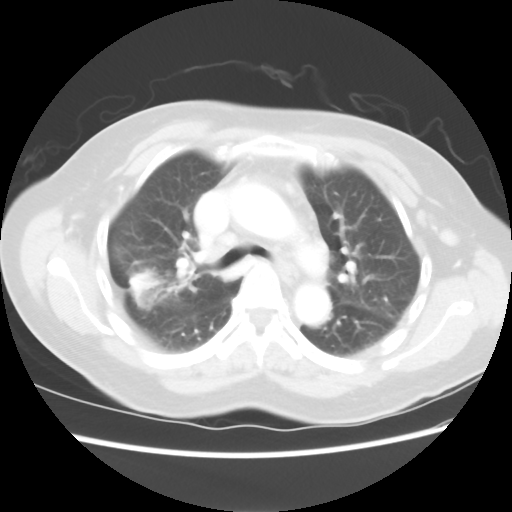
Chest CT, one axial slice. Slice 47 of 80 in the series (ordered by position). Reconstruction kernel STANDARD. 100 kVp. Lung window (W 1500 / L -600 HU). 5 mm slice thickness. 512 × 512 image matrix, field of view 342 × 342 mm. Patient: female, 67 years. Case-level facts recorded for this patient, not image findings: clinical TNM (as recorded): T1c N1 M0.
Outlined on this slice (rectangle marked by the reading radiologist):
- lung tumour (recorded histology: adenocarcinoma): bounding box (x1, y1, x2, y2) in pixels: (124, 257, 176, 330)